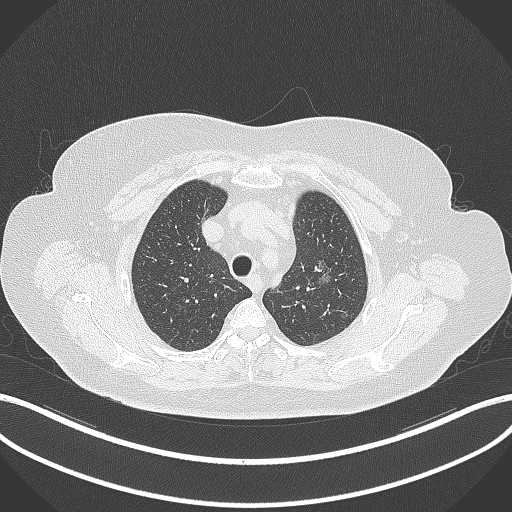
Chest CT, one axial slice; position 271 of 309 along the scan axis; reconstruction kernel B70f; lung window (W 1500 / L -600 HU); 1 mm slice thickness; 512 × 512 image matrix, field of view 400 × 400 mm. Female patient, age 70 years. From the clinical record (not read from this slice): clinical TNM (as recorded): T1c N0 M0.
Annotated regions visible in this slice (rectangle marked by the reading radiologist):
- lung tumour (recorded histology: adenocarcinoma): box from (x=310, y=250) to (x=336, y=293) px